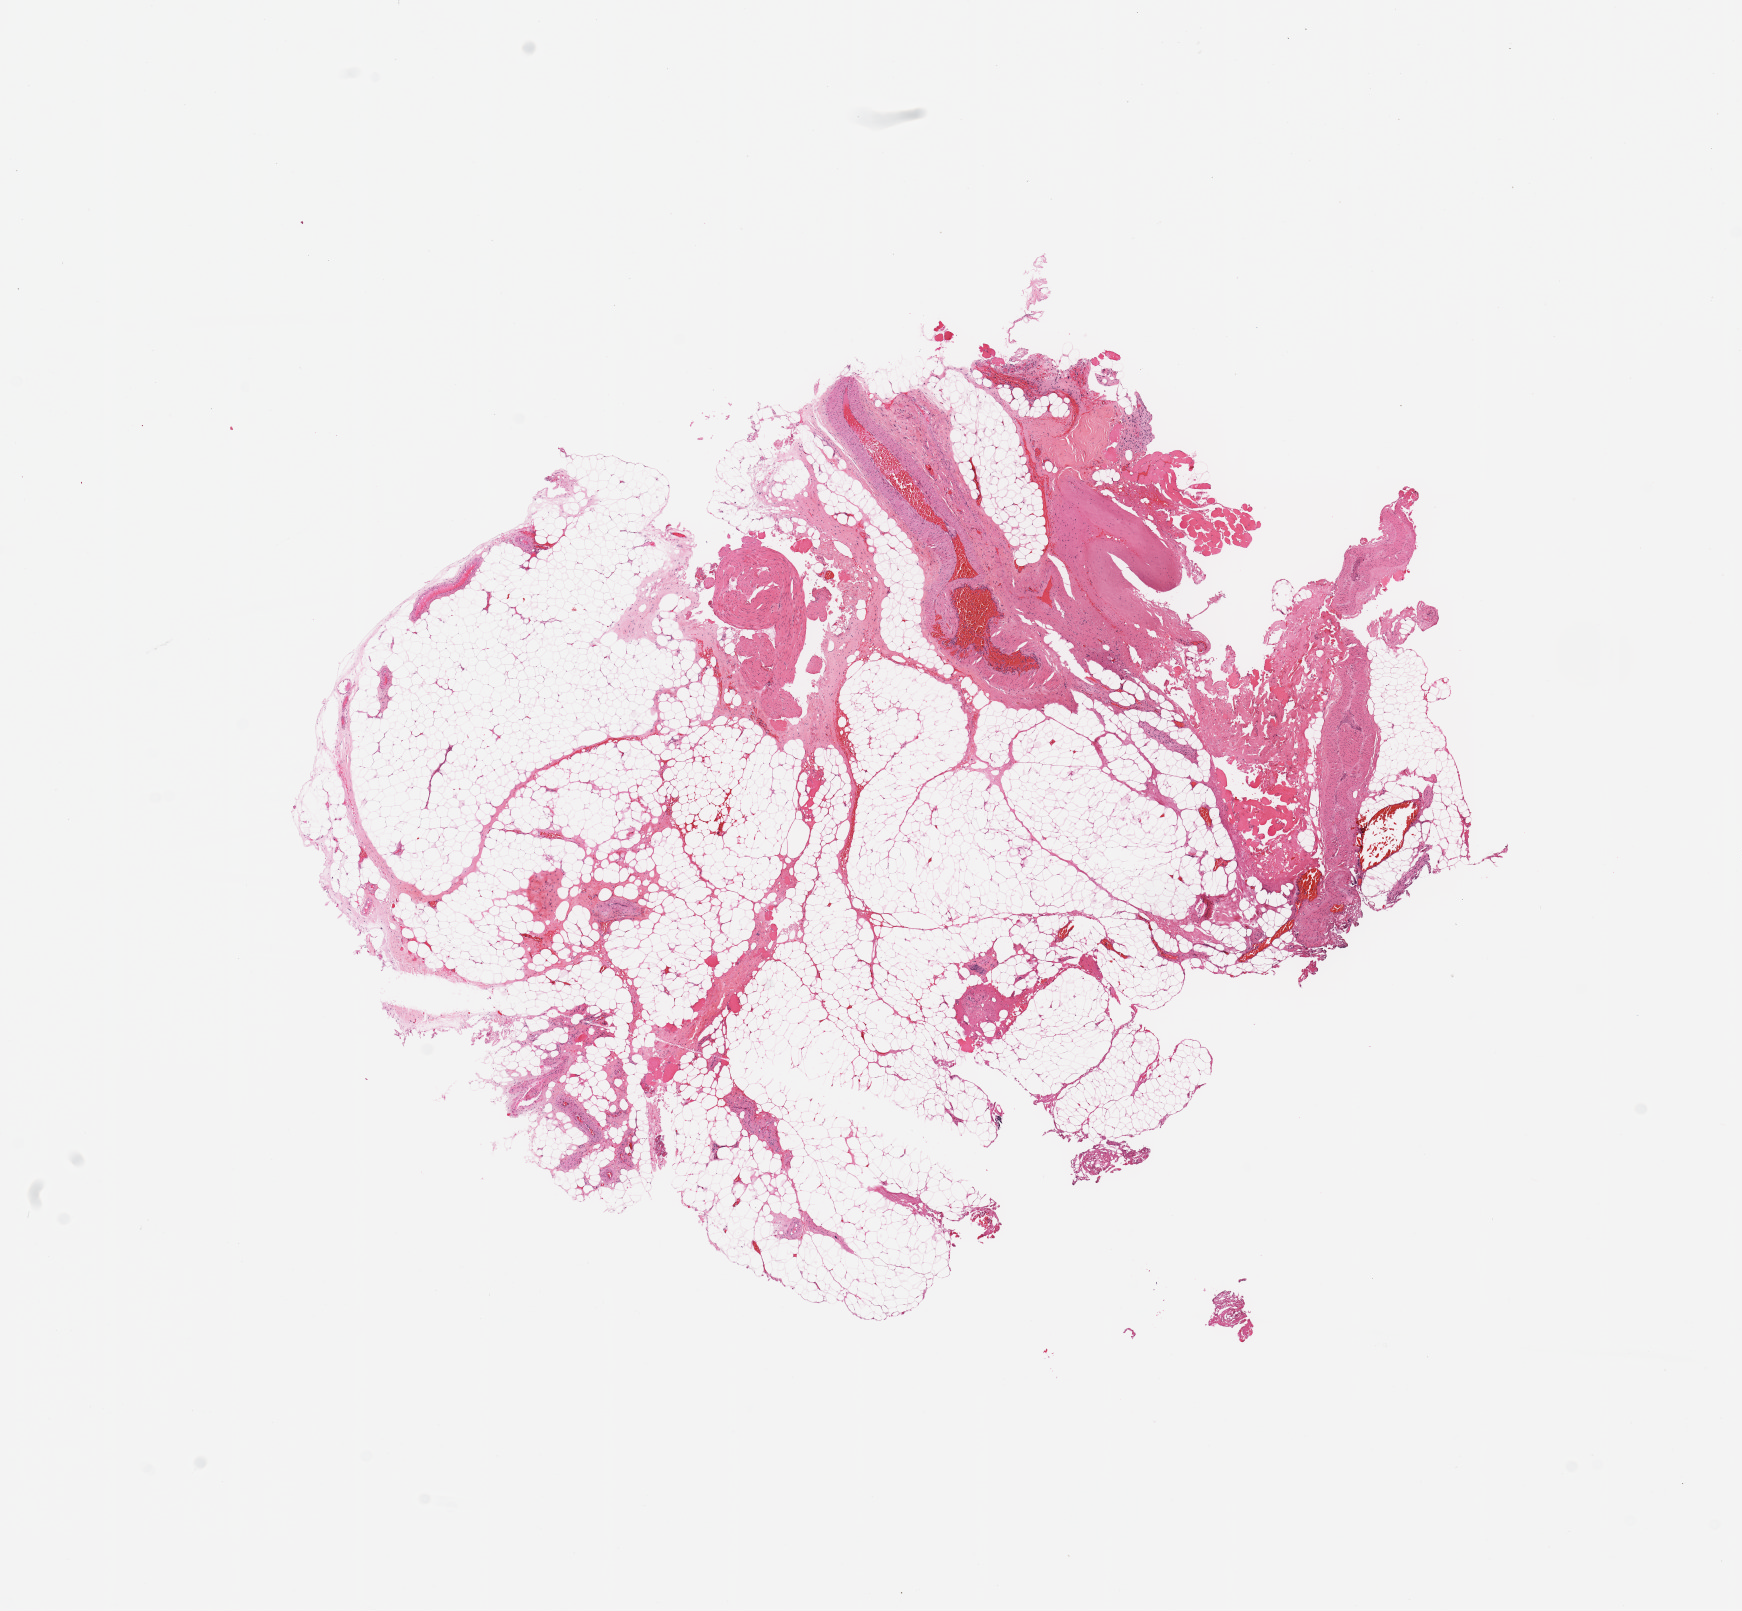
H&E whole-slide image — whole scanned area (about 13.8 x 12.7 mm, from a 20x scan) shown as a low-resolution overview, normal (non-tumour) tissue sample. 52-year-old male patient.
This section: normal (non-tumour) tissue from the same patient. Patient diagnosis (cohort enrolment): sarcoma (site not recorded at cohort level).